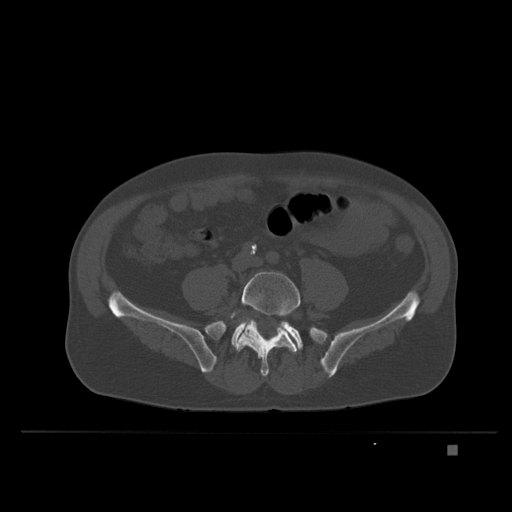
CT including the spine, one axial slice. Slice 54 of 435 in the series (ordered by position). Bone window (W 1800 / L 400 HU). 512 × 512 image matrix. Male patient, age 73 years. Case-level facts recorded for this patient, not image findings: primary cancer: skin.
Annotated regions visible in this slice (semi-automatic segmentation, software-assisted and operator-edited):
- L5 vertebra: bounding box [x1, y1, x2, y2] px = [230, 271, 301, 377]